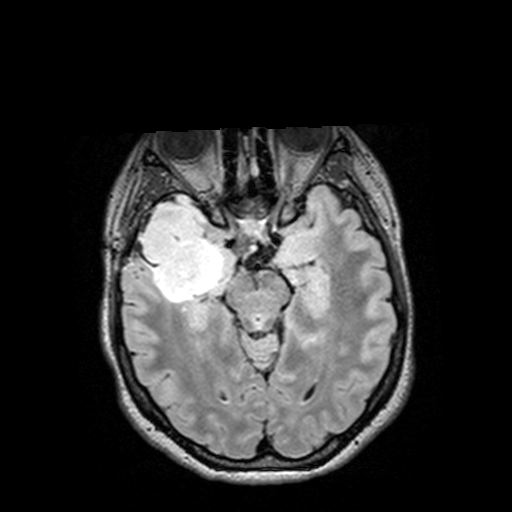
Brain MRI from a brain-tumour surgery series, one axial slice. Slice 87 of 144 in the series (ordered by position). T2 FLAIR. 1 mm slice thickness. 512 × 512 image matrix, field of view 250 × 250 mm. Case-level facts recorded for this patient, not image findings: histopathology: Astrocytoma; WHO grade: 3; IDH mutation: yes; tumour location: Right Insular Temporal.
Annotated regions visible in this slice (outlined manually by an expert reader):
- tumour: bounding box (x1, y1, x2, y2) in pixels: (126, 195, 232, 303)